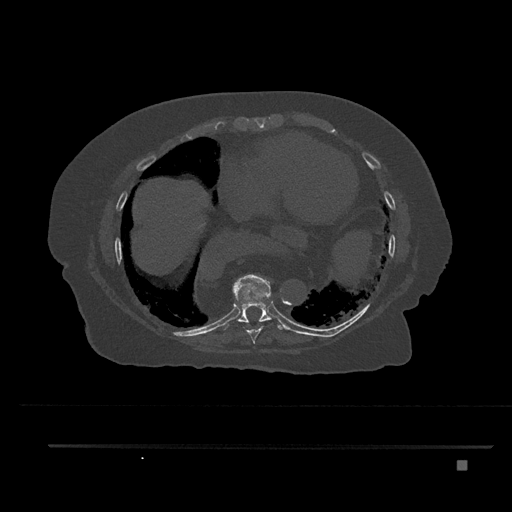
CT including the spine, one axial slice. Position 419 of 797 along the scan axis. 120 kVp. Bone window (W 1800 / L 400 HU). 512 × 512 image matrix, field of view 437 × 437 mm. Patient: female, 76 years. From the clinical record (not read from this slice): primary cancer: lung.
Structures marked on this image (semi-automatically segmented with operator editing):
- T8 vertebra: box from (x=240, y=322) to (x=263, y=346) px
- T9 vertebra: (x=223, y=274)–(x=285, y=330)